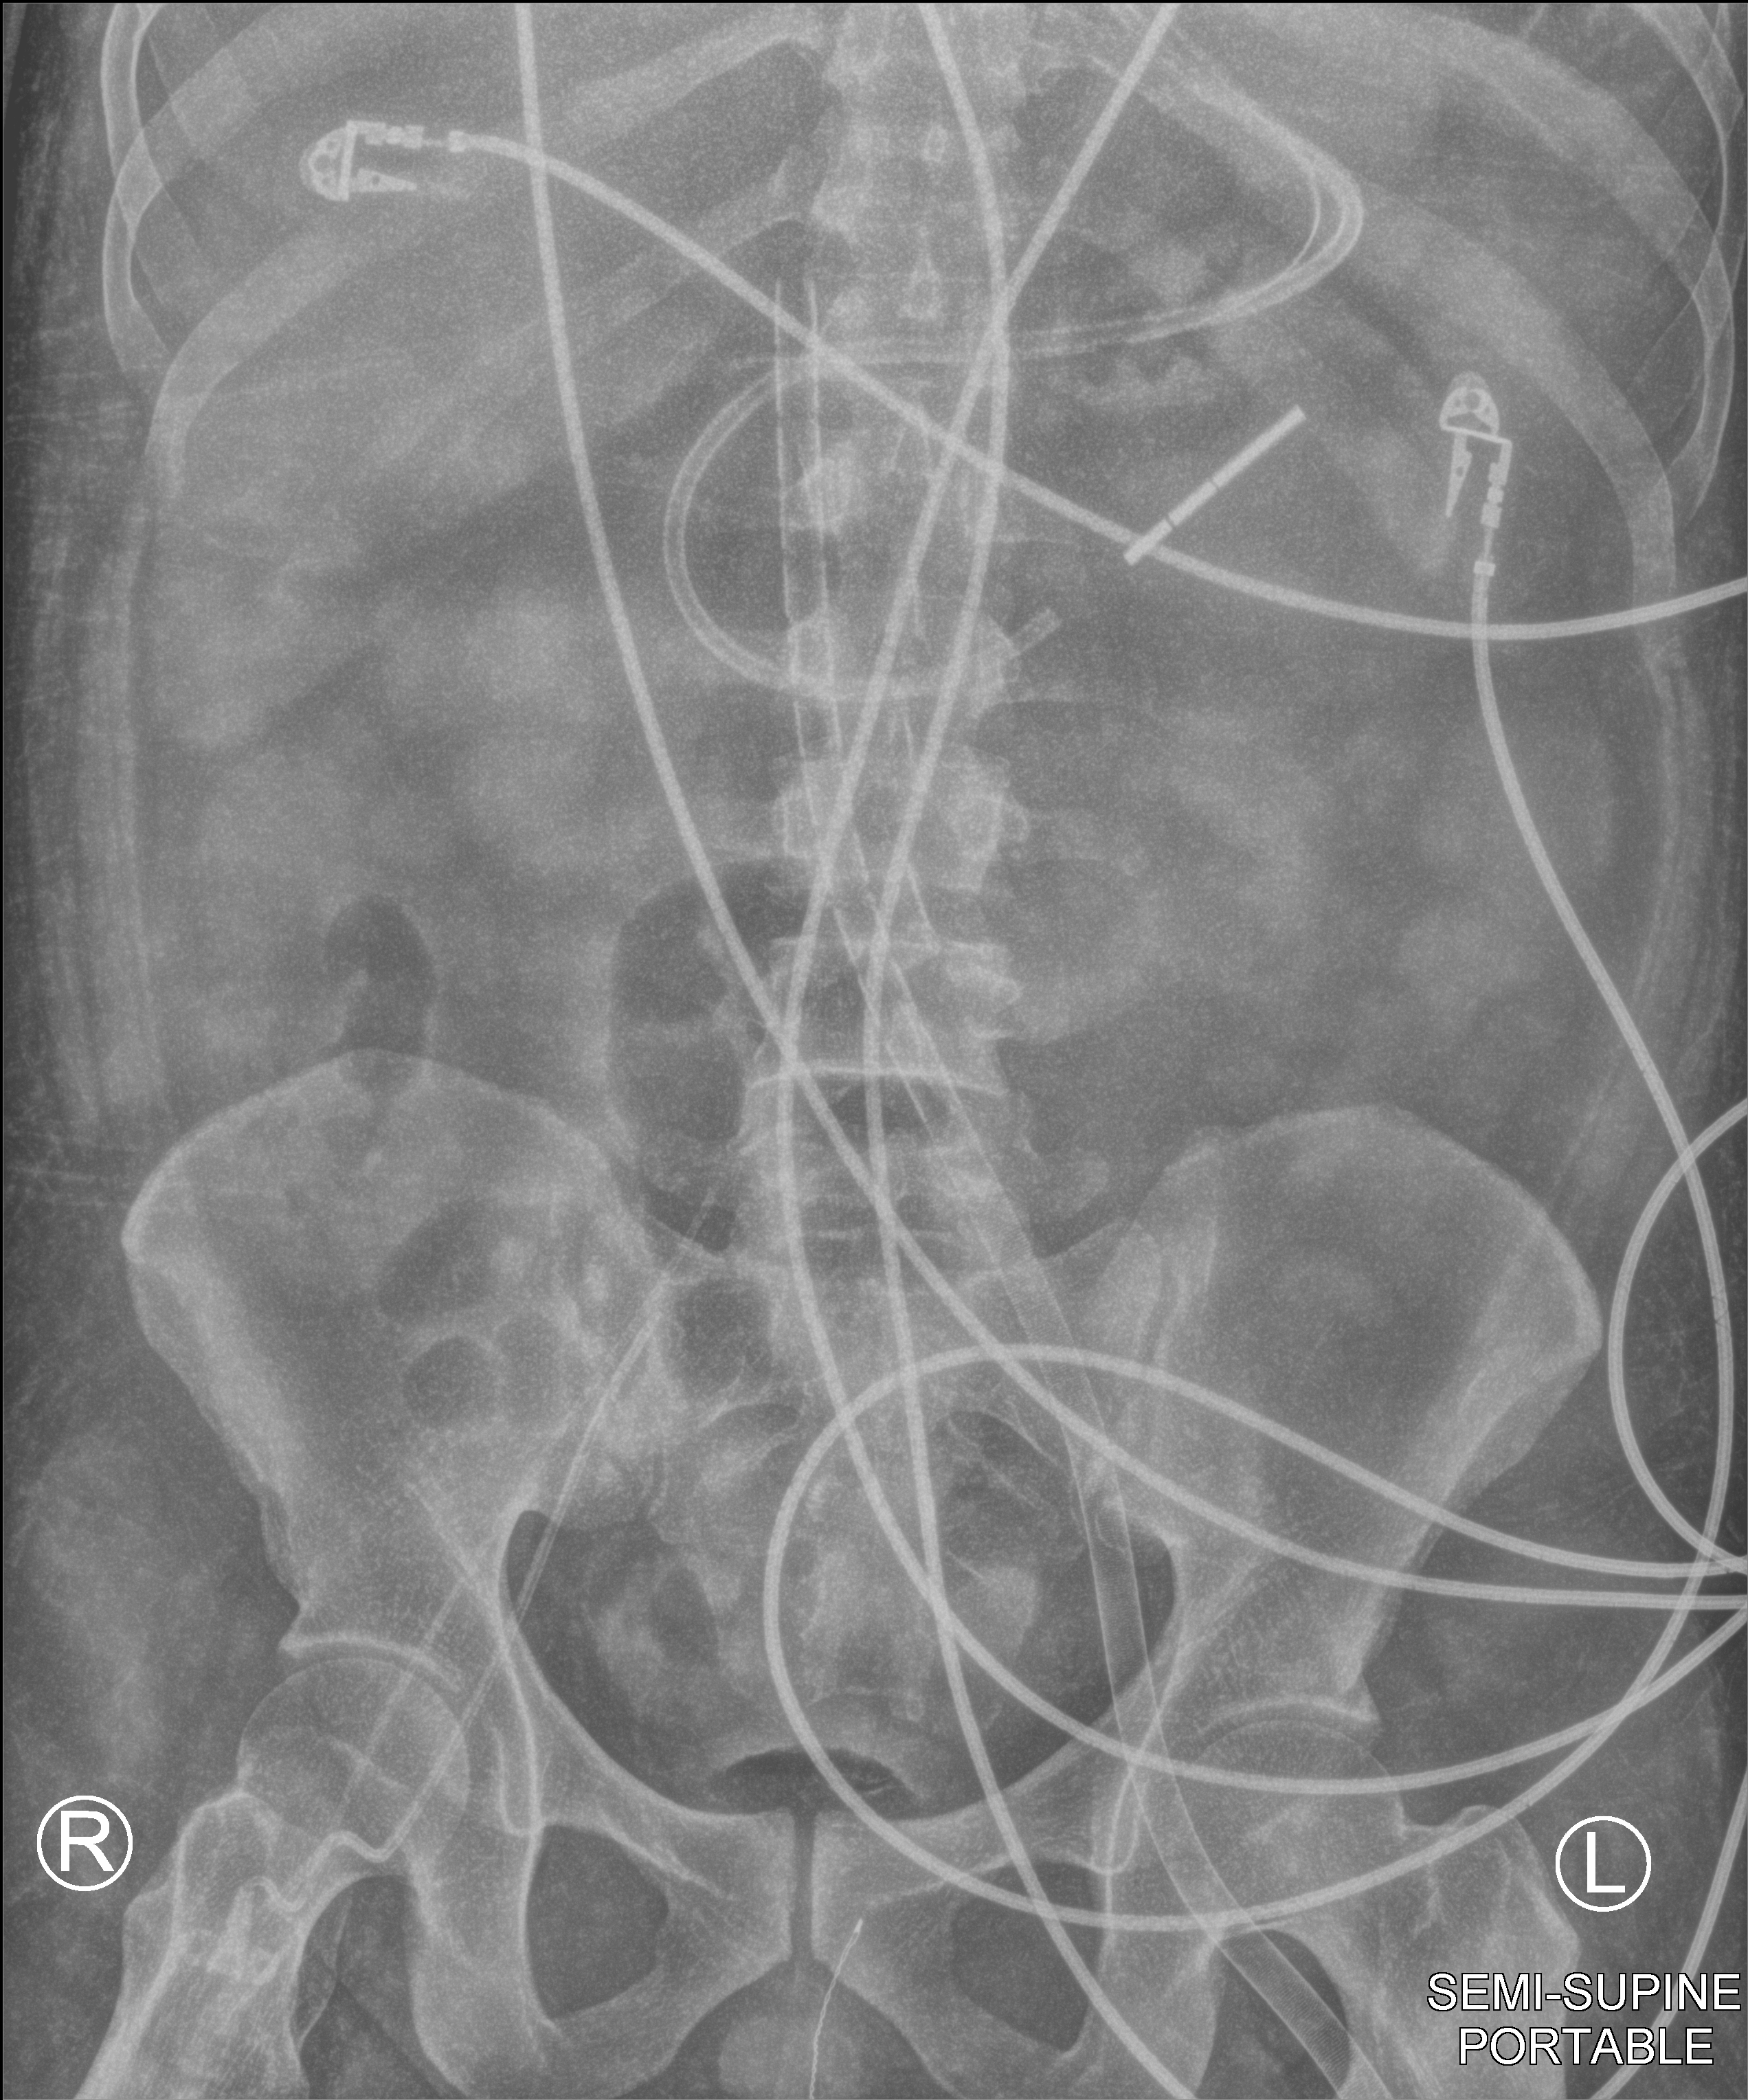
Bedside abdomen radiograph (computed radiography). Adult patient hospitalised with COVID-19, age 18–59 years.
From the hospital-stay record, not from the radiograph (when in the stay this image was taken is not recorded):
- mechanically ventilated during this hospital stay: yes